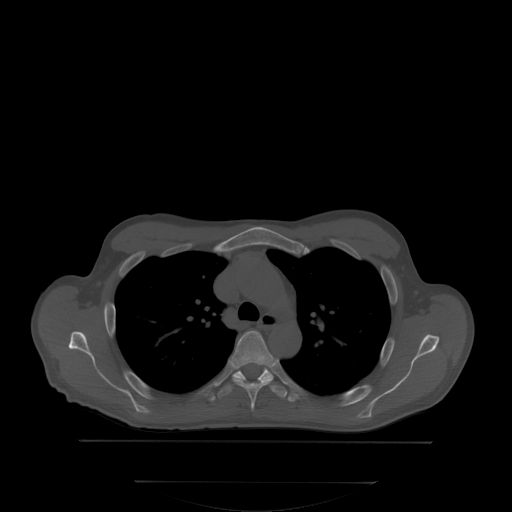
CT including the spine, one axial slice; position 254 of 350 along the scan axis; bone window (W 1800 / L 400 HU); 2.5 mm slice thickness; 512 × 512 image matrix. Male patient, age 58 years. Case-level facts recorded for this patient, not image findings: primary cancer: prostate; vertebrae with lytic lesions (as recorded): L1.
Annotated regions visible in this slice (semi-automatically segmented with operator editing):
- T4 vertebra: box from (x=231, y=330) to (x=275, y=409) px
- T5 vertebra: (x=217, y=365)–(x=300, y=399)